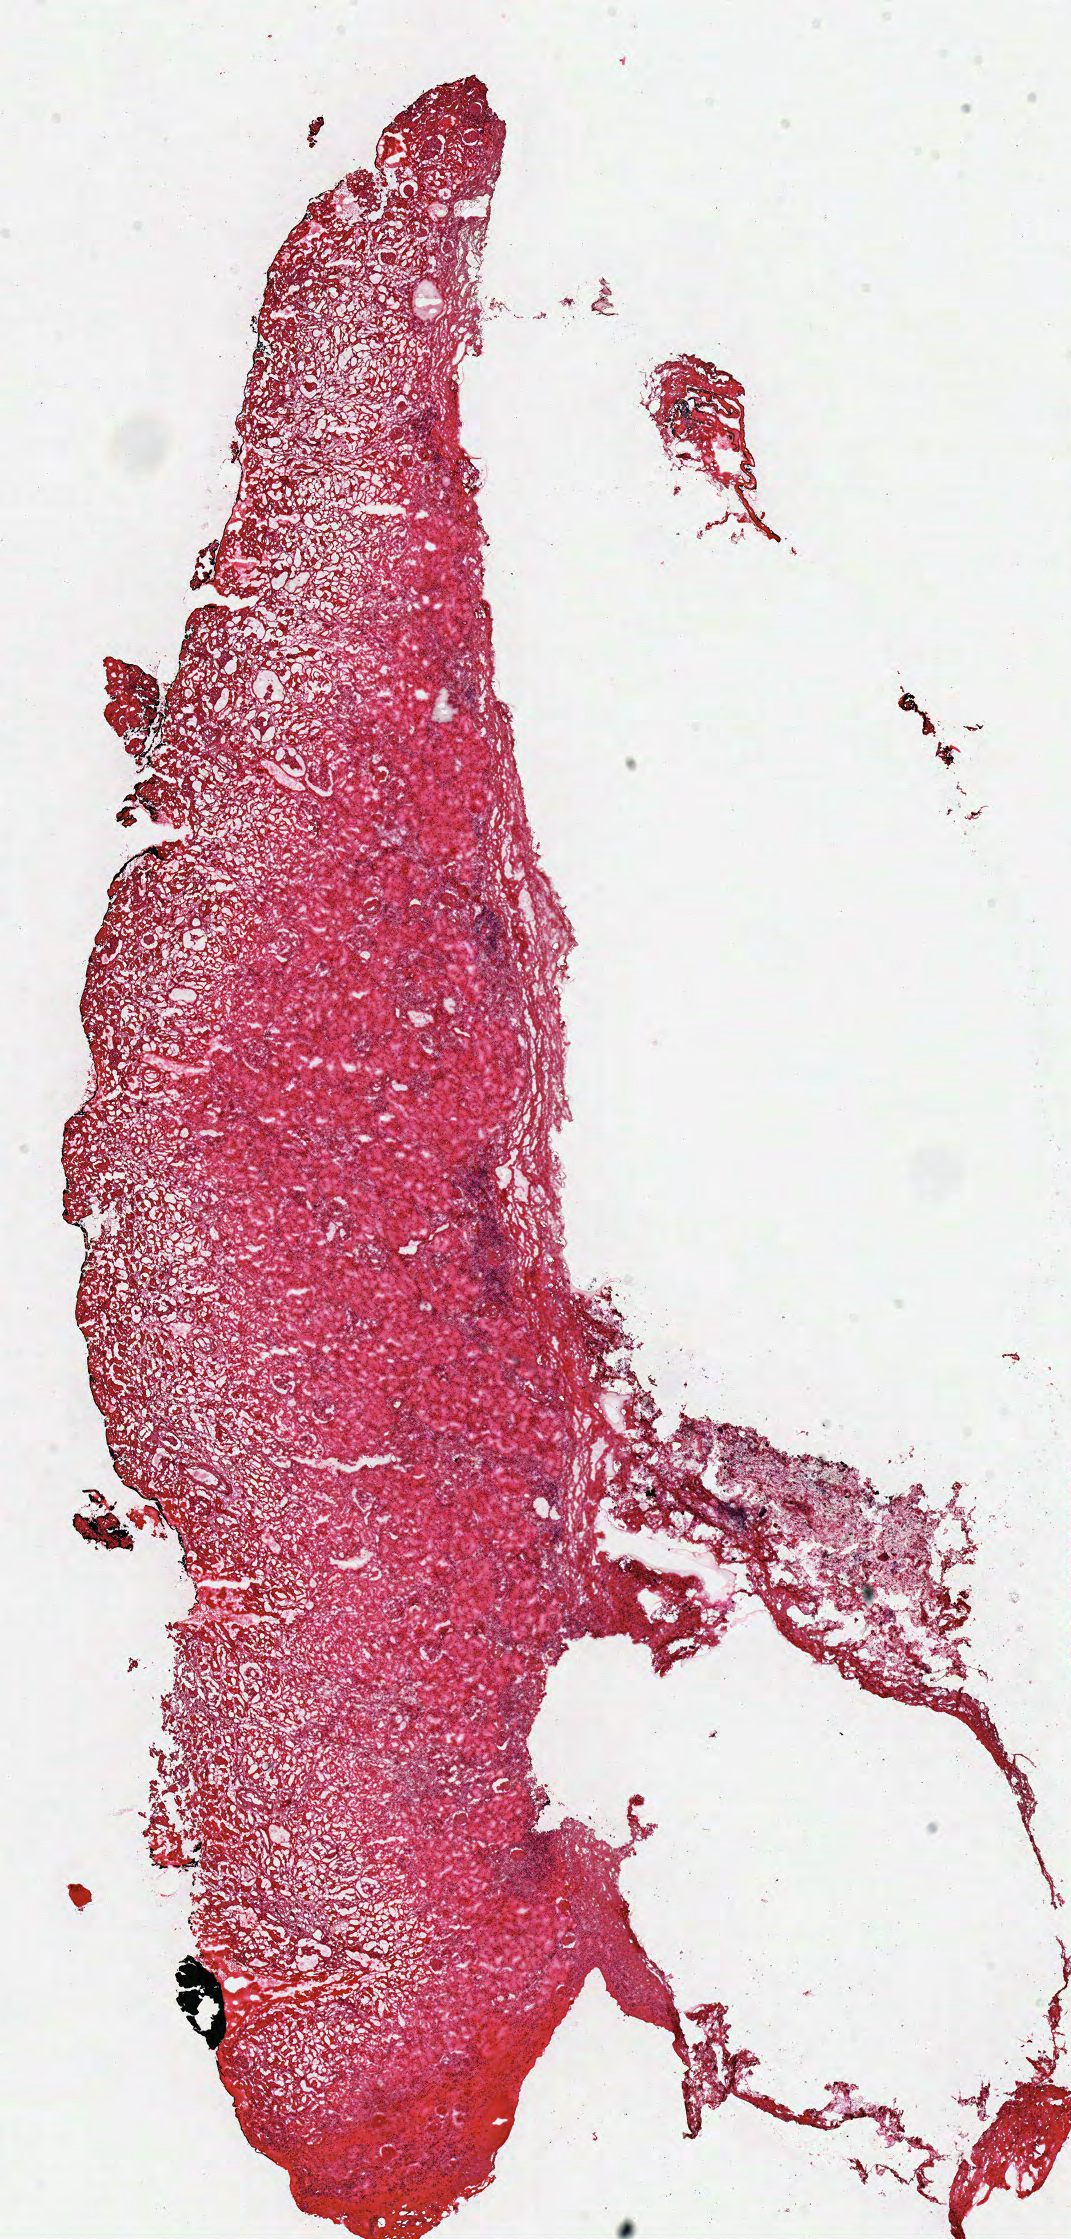
Digitized Hematoxylin and eosin (H&E) stained tissue section (whole slide), a low-resolution overview of the entire scanned area, about 8.4 x 17.6 mm (slide scanned at 40x). Frozen section from the top of the tissue portion. Kidney, solid tissue normal (non-tumour tissue) sample. Male, age 75 years at initial diagnosis.
This section: solid tissue normal sample (biorepository sample class). Patient diagnosis: Papillary adenocarcinoma, NOS.